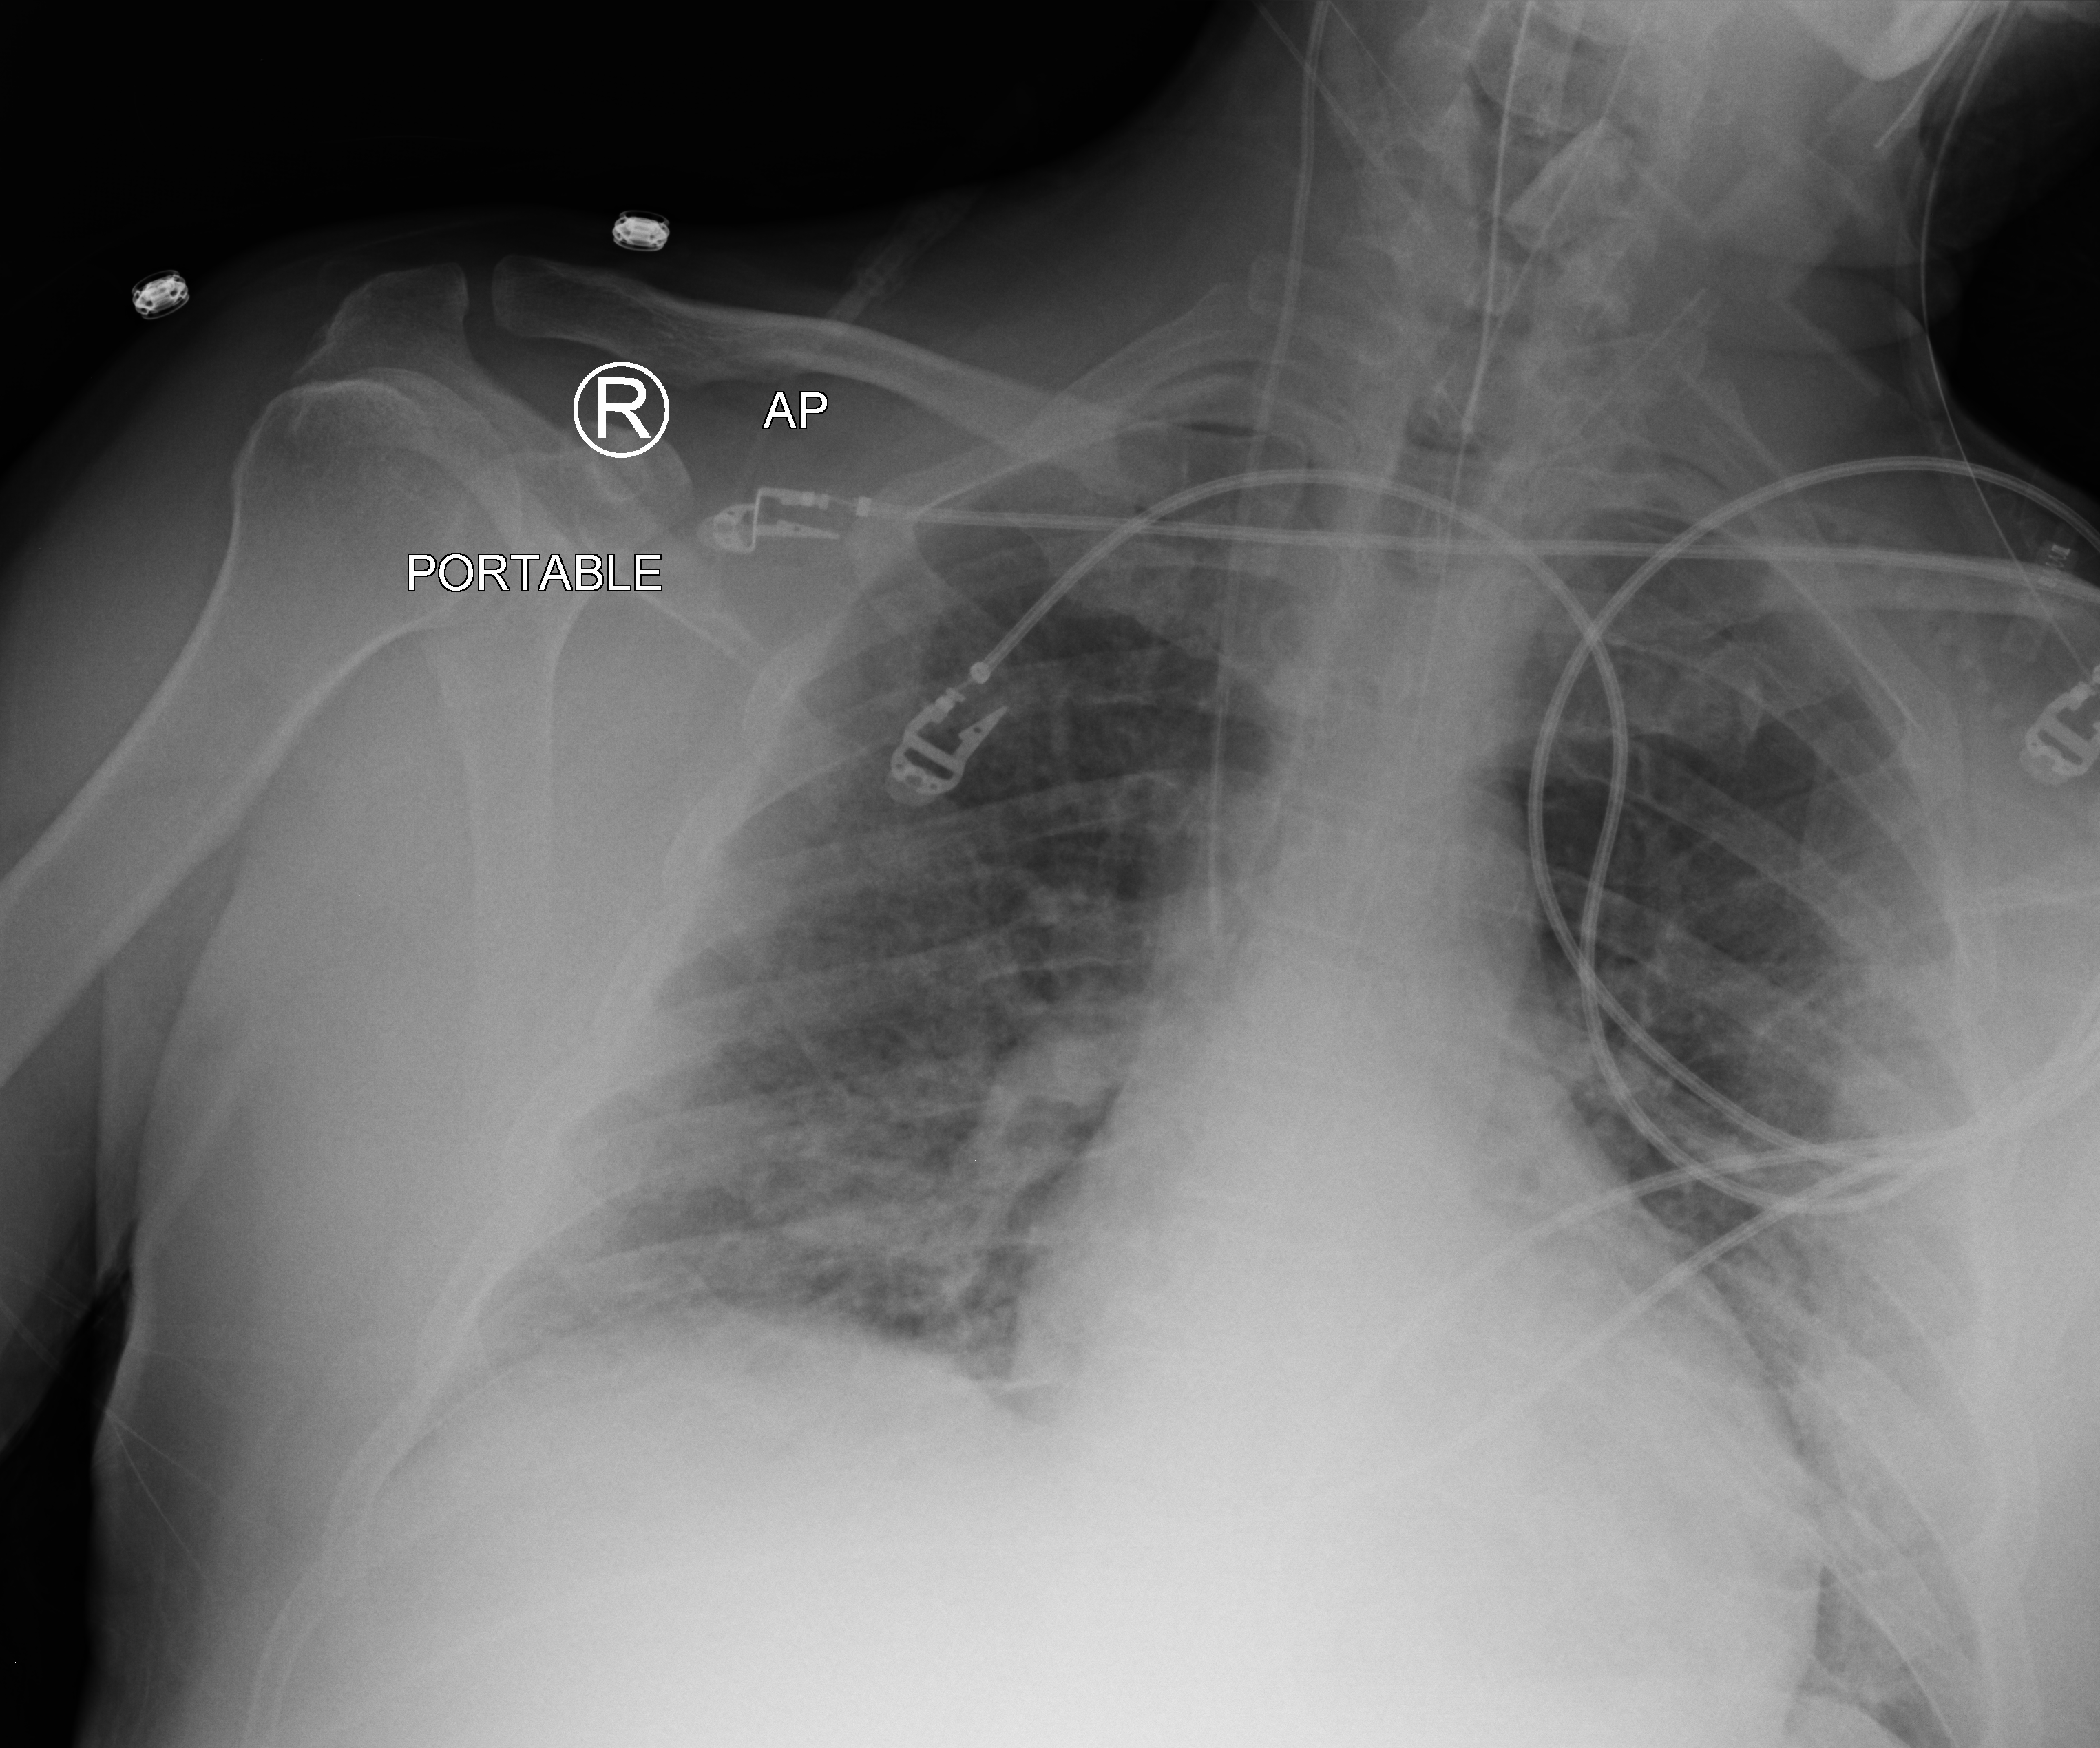
Bedside chest radiograph (computed radiography). Patient hospitalised with COVID-19; male, aged 18–59 years.
From the hospital-stay record, not from the radiograph (when in the stay this image was taken is not recorded): length of hospital stay: 32 days.